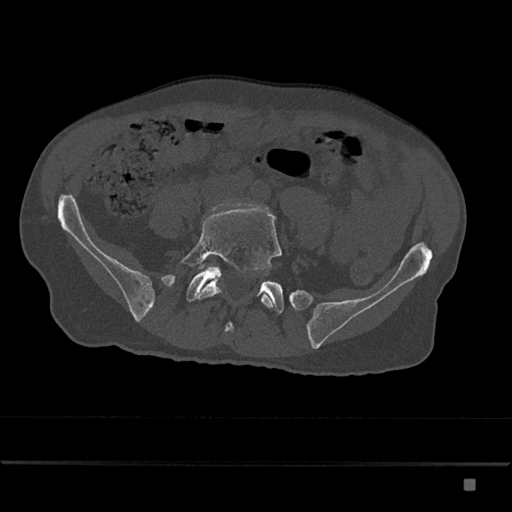
CT including the spine, one axial slice; position 265 of 797 along the scan axis; reconstruction kernel Br40s/3; bone window (W 1800 / L 400 HU); 0.5 mm slice thickness; 512 × 512 image matrix. Male patient, age 72 years. Case-level facts recorded for this patient, not image findings: primary cancer: prostate.
Structures marked on this image (semi-automatic segmentation, software-assisted and operator-edited):
- L5 vertebra: bounding box (x1, y1, x2, y2) in pixels: (181, 208, 282, 308)